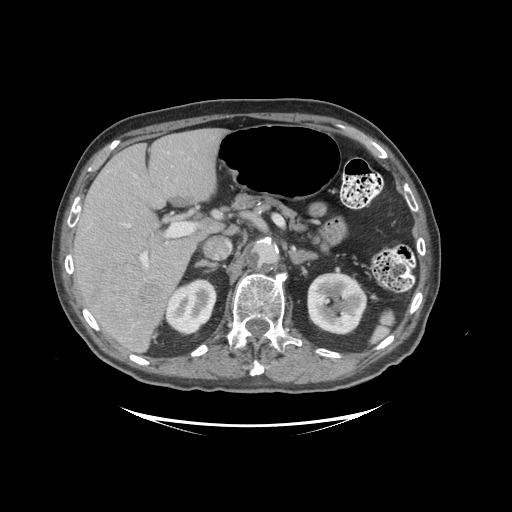
Contrast-enhanced abdominal CT (liver protocol), one axial slice. Slice 59 of 99 in the series (ordered by position). 140 kVp. Soft-tissue window (W 400 / L 40 HU). 2.5 mm slice thickness. 512 × 512 image matrix. From the clinical record (not read from this slice): diagnosis: hepatocellular carcinoma (patient treated with transarterial chemoembolisation; whether this scan precedes or follows treatment is not stated here); TNM stage (as recorded): Stage-I; Child-Pugh class: A; tumour differentiation: moderately differentiated.
Structures marked on this image (semi-automatic segmentation, software-assisted and operator-edited):
- liver parenchyma outside the tumour (the mass and vessels are separate outlines, so this box may not span the whole liver): bounding box <72,128,224,350> (left, top, right, bottom; pixels)
- mass: <78,253,171,347>
- liver vessels: <77,218,195,267>